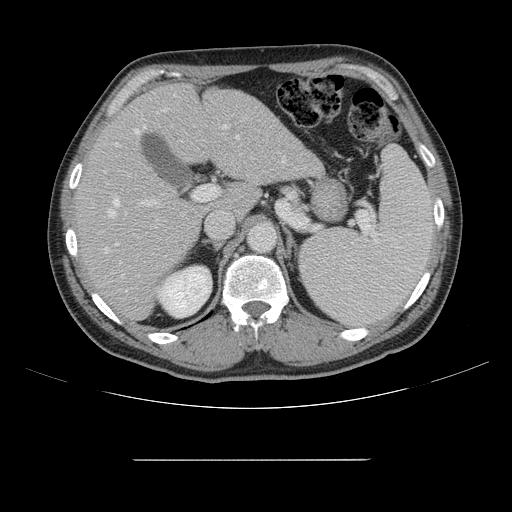
Contrast-enhanced abdominal CT, one axial slice. Position 96 of 164 along the scan axis. Intravenous contrast given. Soft-tissue window (W 400 / L 40 HU). 2.5 mm slice thickness. 512 × 512 image matrix, field of view 404 × 404 mm. Male patient, age 54 years. Case-level facts recorded for this patient, not image findings: diagnosis: colorectal cancer liver metastases, imaged before liver resection; multiple liver metastases: yes; largest metastasis: 1 cm.
Structures marked on this image (outlined manually by an expert reader):
- hepatic veins: bounding box (x1, y1, x2, y2) in pixels: (105, 129, 284, 277)
- liver: (77, 84, 320, 320)
- planned liver remnant (the part of the liver to remain after resection): (77, 84, 234, 319)
- portal vein (with intrahepatic branches): (116, 94, 229, 205)